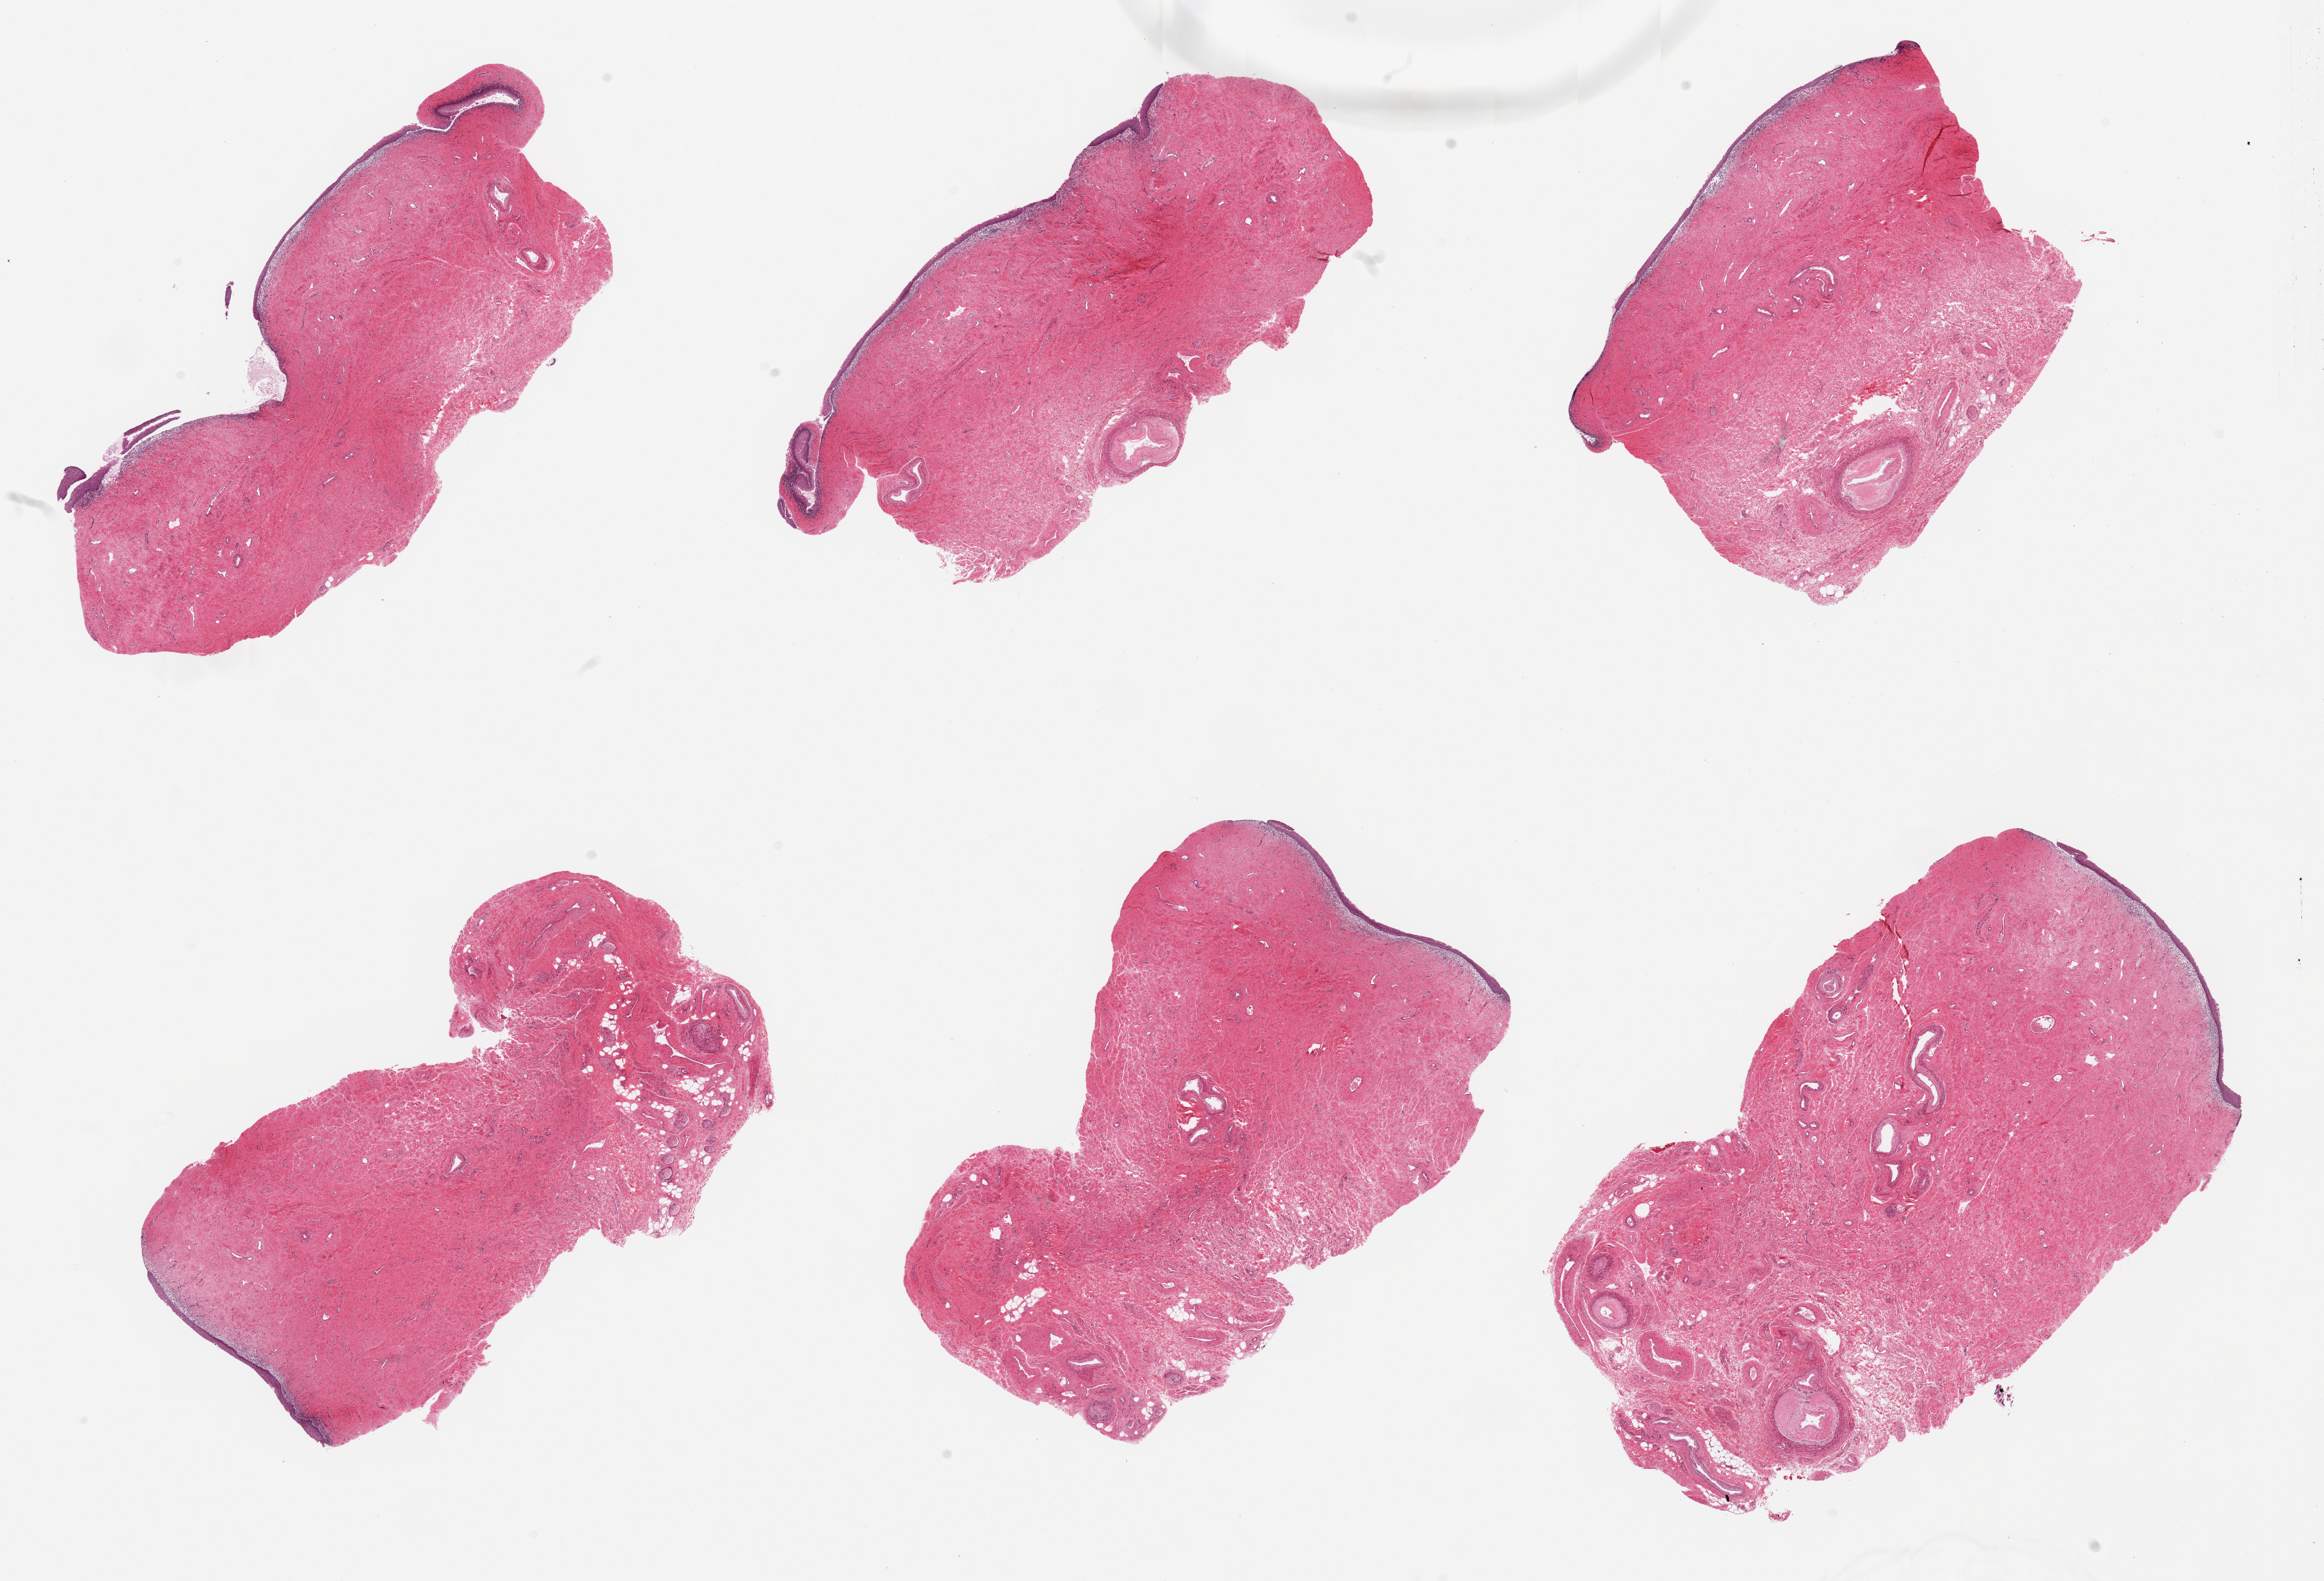
Digitized H&E-stained section — low-resolution overview of the scanned area, about 27.6 x 18.8 mm, PAXgene-fixed, paraffin-embedded tissue, sampled site (target tissue): vagina, tissue donor sample.
- pathologist's review note for this sample: 2 pieces, squamous mucosa is ~75 microns. Diffuse mild chronic vaginitis